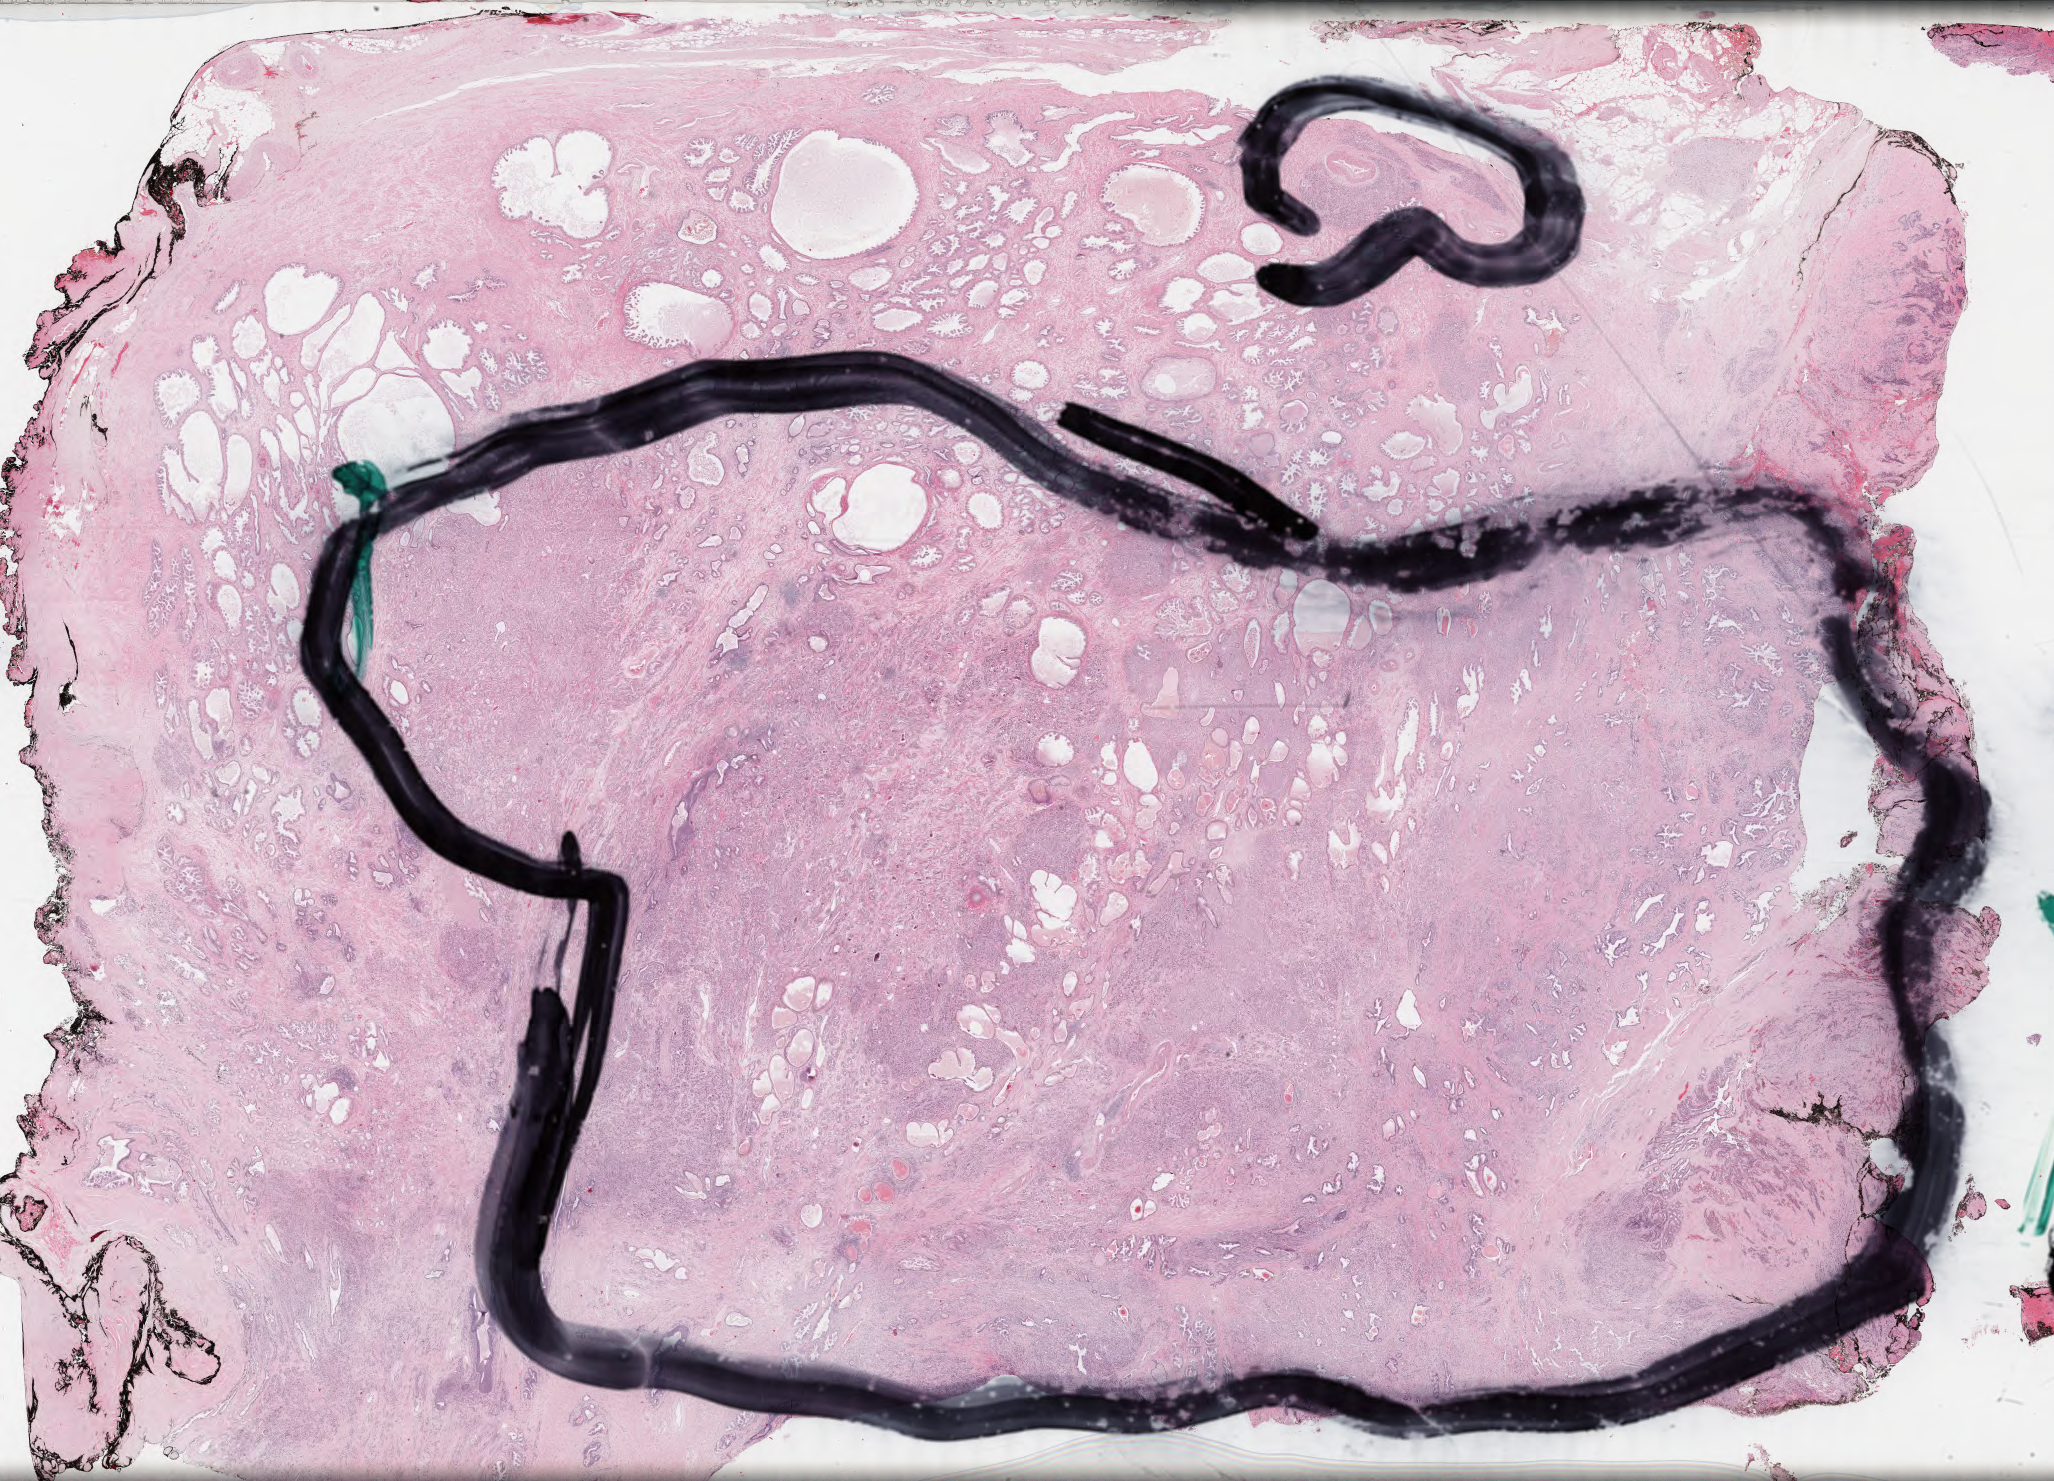
Whole-slide histology image, H&E-stained, shown as a low-resolution overview of the whole scanned area (about 32.7 x 23.6 mm, slide scanned at 40x); FFPE section; sample: primary tumour, prostate. Patient: male, age at initial diagnosis 63 years. Gleason score: 9 (4+5).
Histologic diagnosis: Adenocarcinoma, NOS (prostate gland). Laterality: bilateral. Lymph nodes positive (case pathology): 0 of 1 examined.